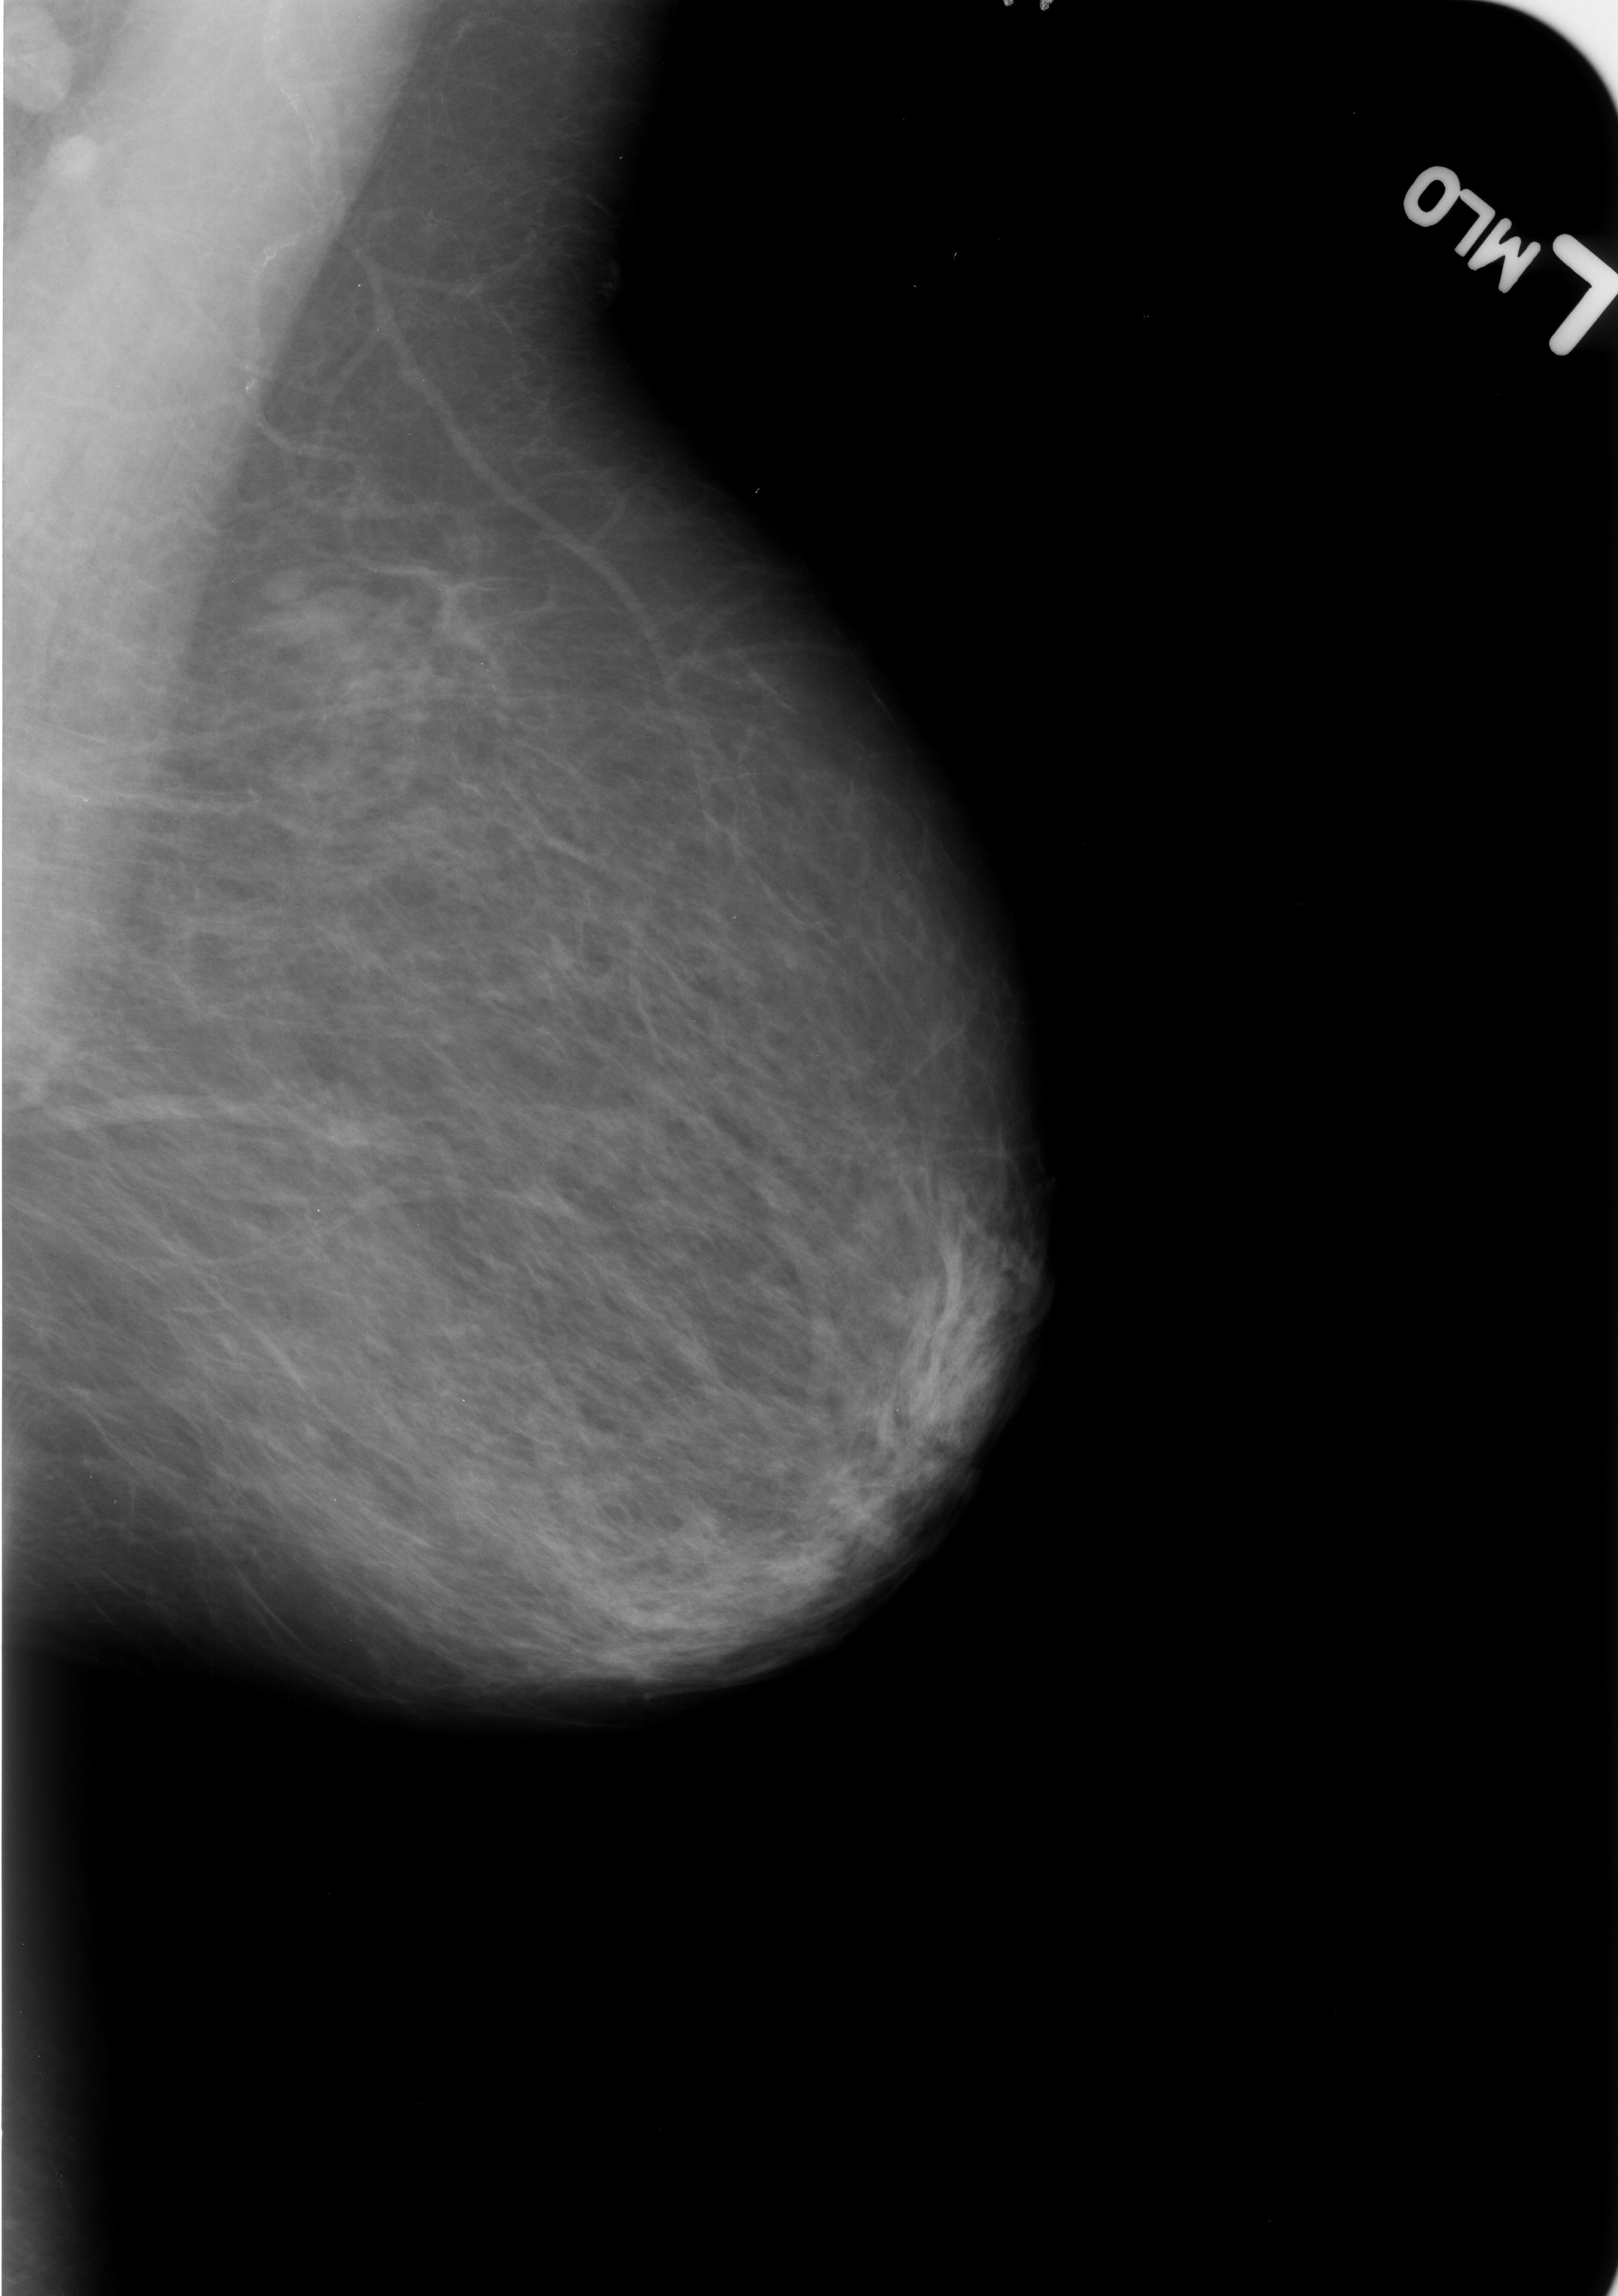
Mammogram (digitized film); left breast; mediolateral oblique (MLO) view; breast composition: almost entirely fatty (BI-RADS density category 1 of 4); 1618 × 2296 image matrix.
Expert-marked regions of interest on this film, with their recorded descriptors:
- calcifications, morphology vascular; BI-RADS assessment category 2; subtlety rating 4 on a 1 (subtle) to 5 (obvious) scale; outcome (as recorded, no biopsy): benign without callback (not worked up further): bounding box <203,10,372,475> (left, top, right, bottom; pixels)